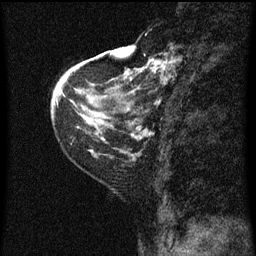
Breast MRI (dynamic contrast-enhanced), one sagittal slice. Slice 17 of 60 in the series (ordered by position). Dynamic contrast-enhanced series, image 2 of 3 at this slice position (ordered by acquisition). 1.5 T. TE 4.2 ms, TR 8 ms. 256 × 256 image matrix. Patient: female, 48 years.
Outlined on this slice (semi-automatic segmentation, software-assisted and operator-edited):
- analysis volume of interest (the breast-tissue region the enhancement analysis was run in; not a lesion): box from (x=128, y=54) to (x=175, y=125) px
- tumour enhancement mask (voxels above the 70 % enhancement threshold inside the analysis volume of interest): (x=128, y=58)–(x=175, y=105)